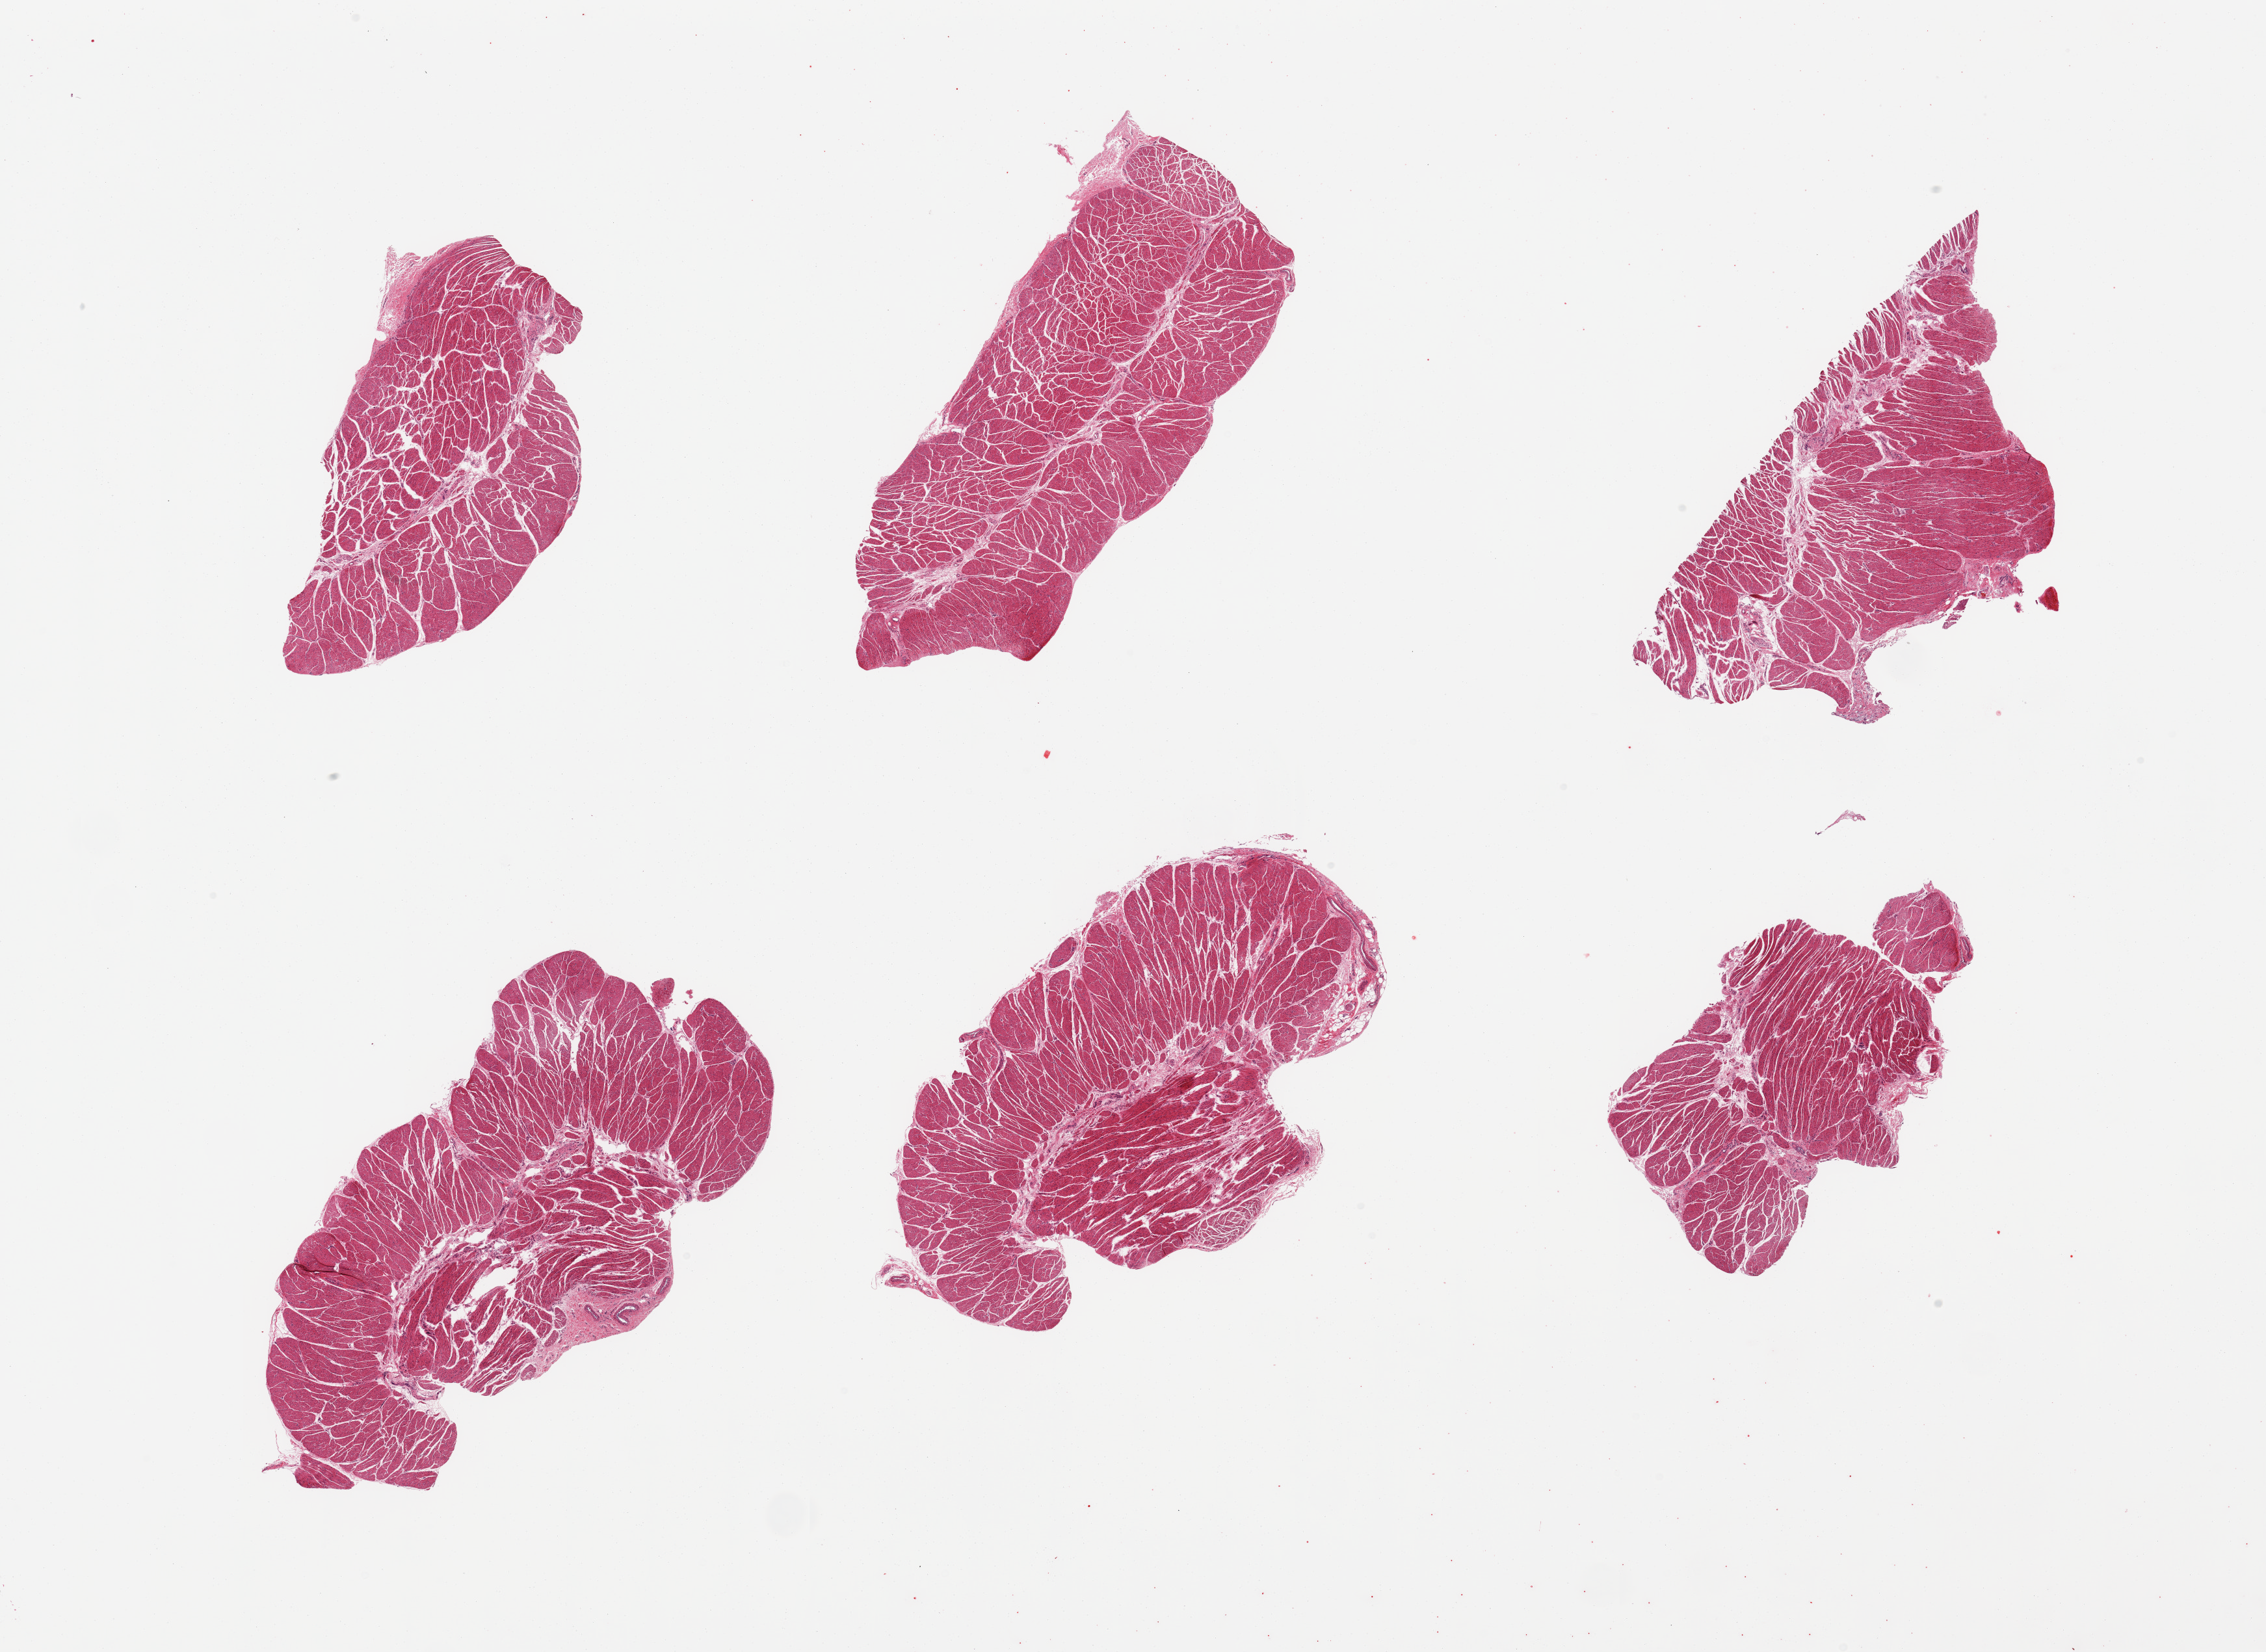
H&E whole-slide image — whole scanned area (about 27.6 x 20.1 mm, slide scanned at 20x) shown as a low-resolution overview. PAXgene-fixed, paraffin-embedded tissue. Section of gastroesophageal junction (target tissue). Donor tissue sample. Donor: female.
Review note (as recorded): 6 pieces; well trimmed target muscularis.